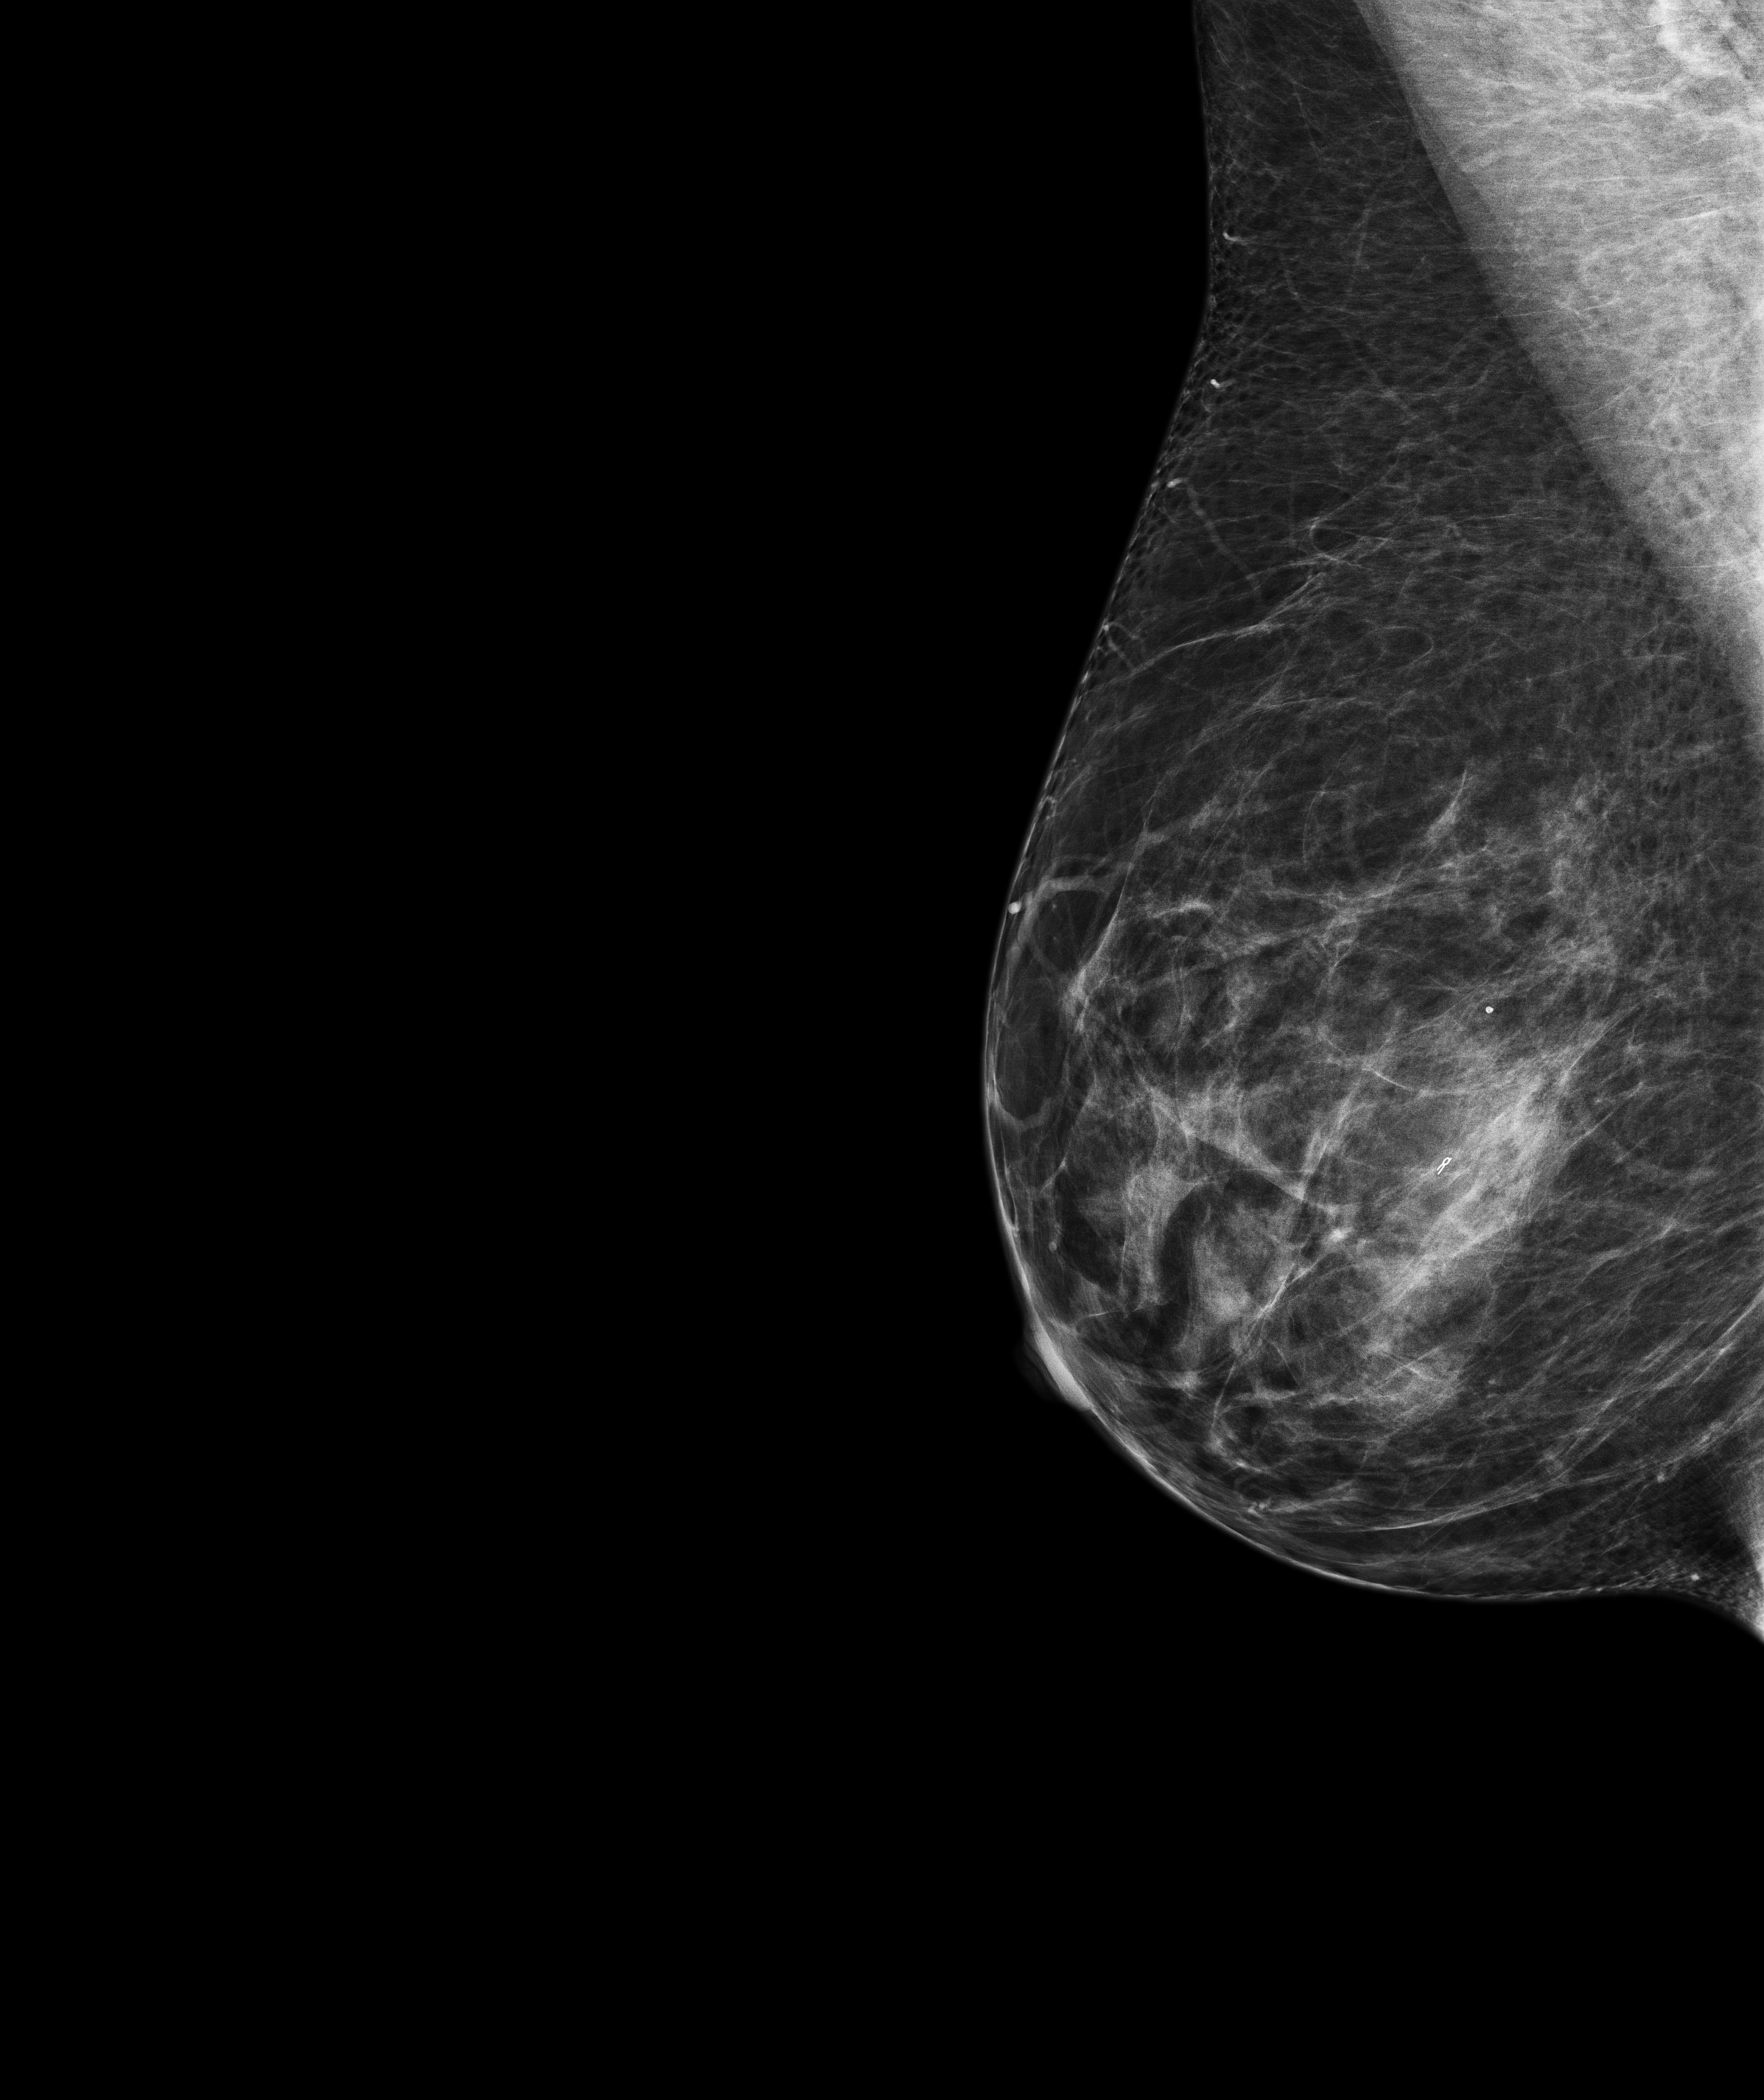
Screening examination; compressed breast thickness 60.5 mm; system: Senographe Pristina. Patient: female, 49 years.
Image type: full-field digital mammogram. Breast: right. Projection: MLO view.